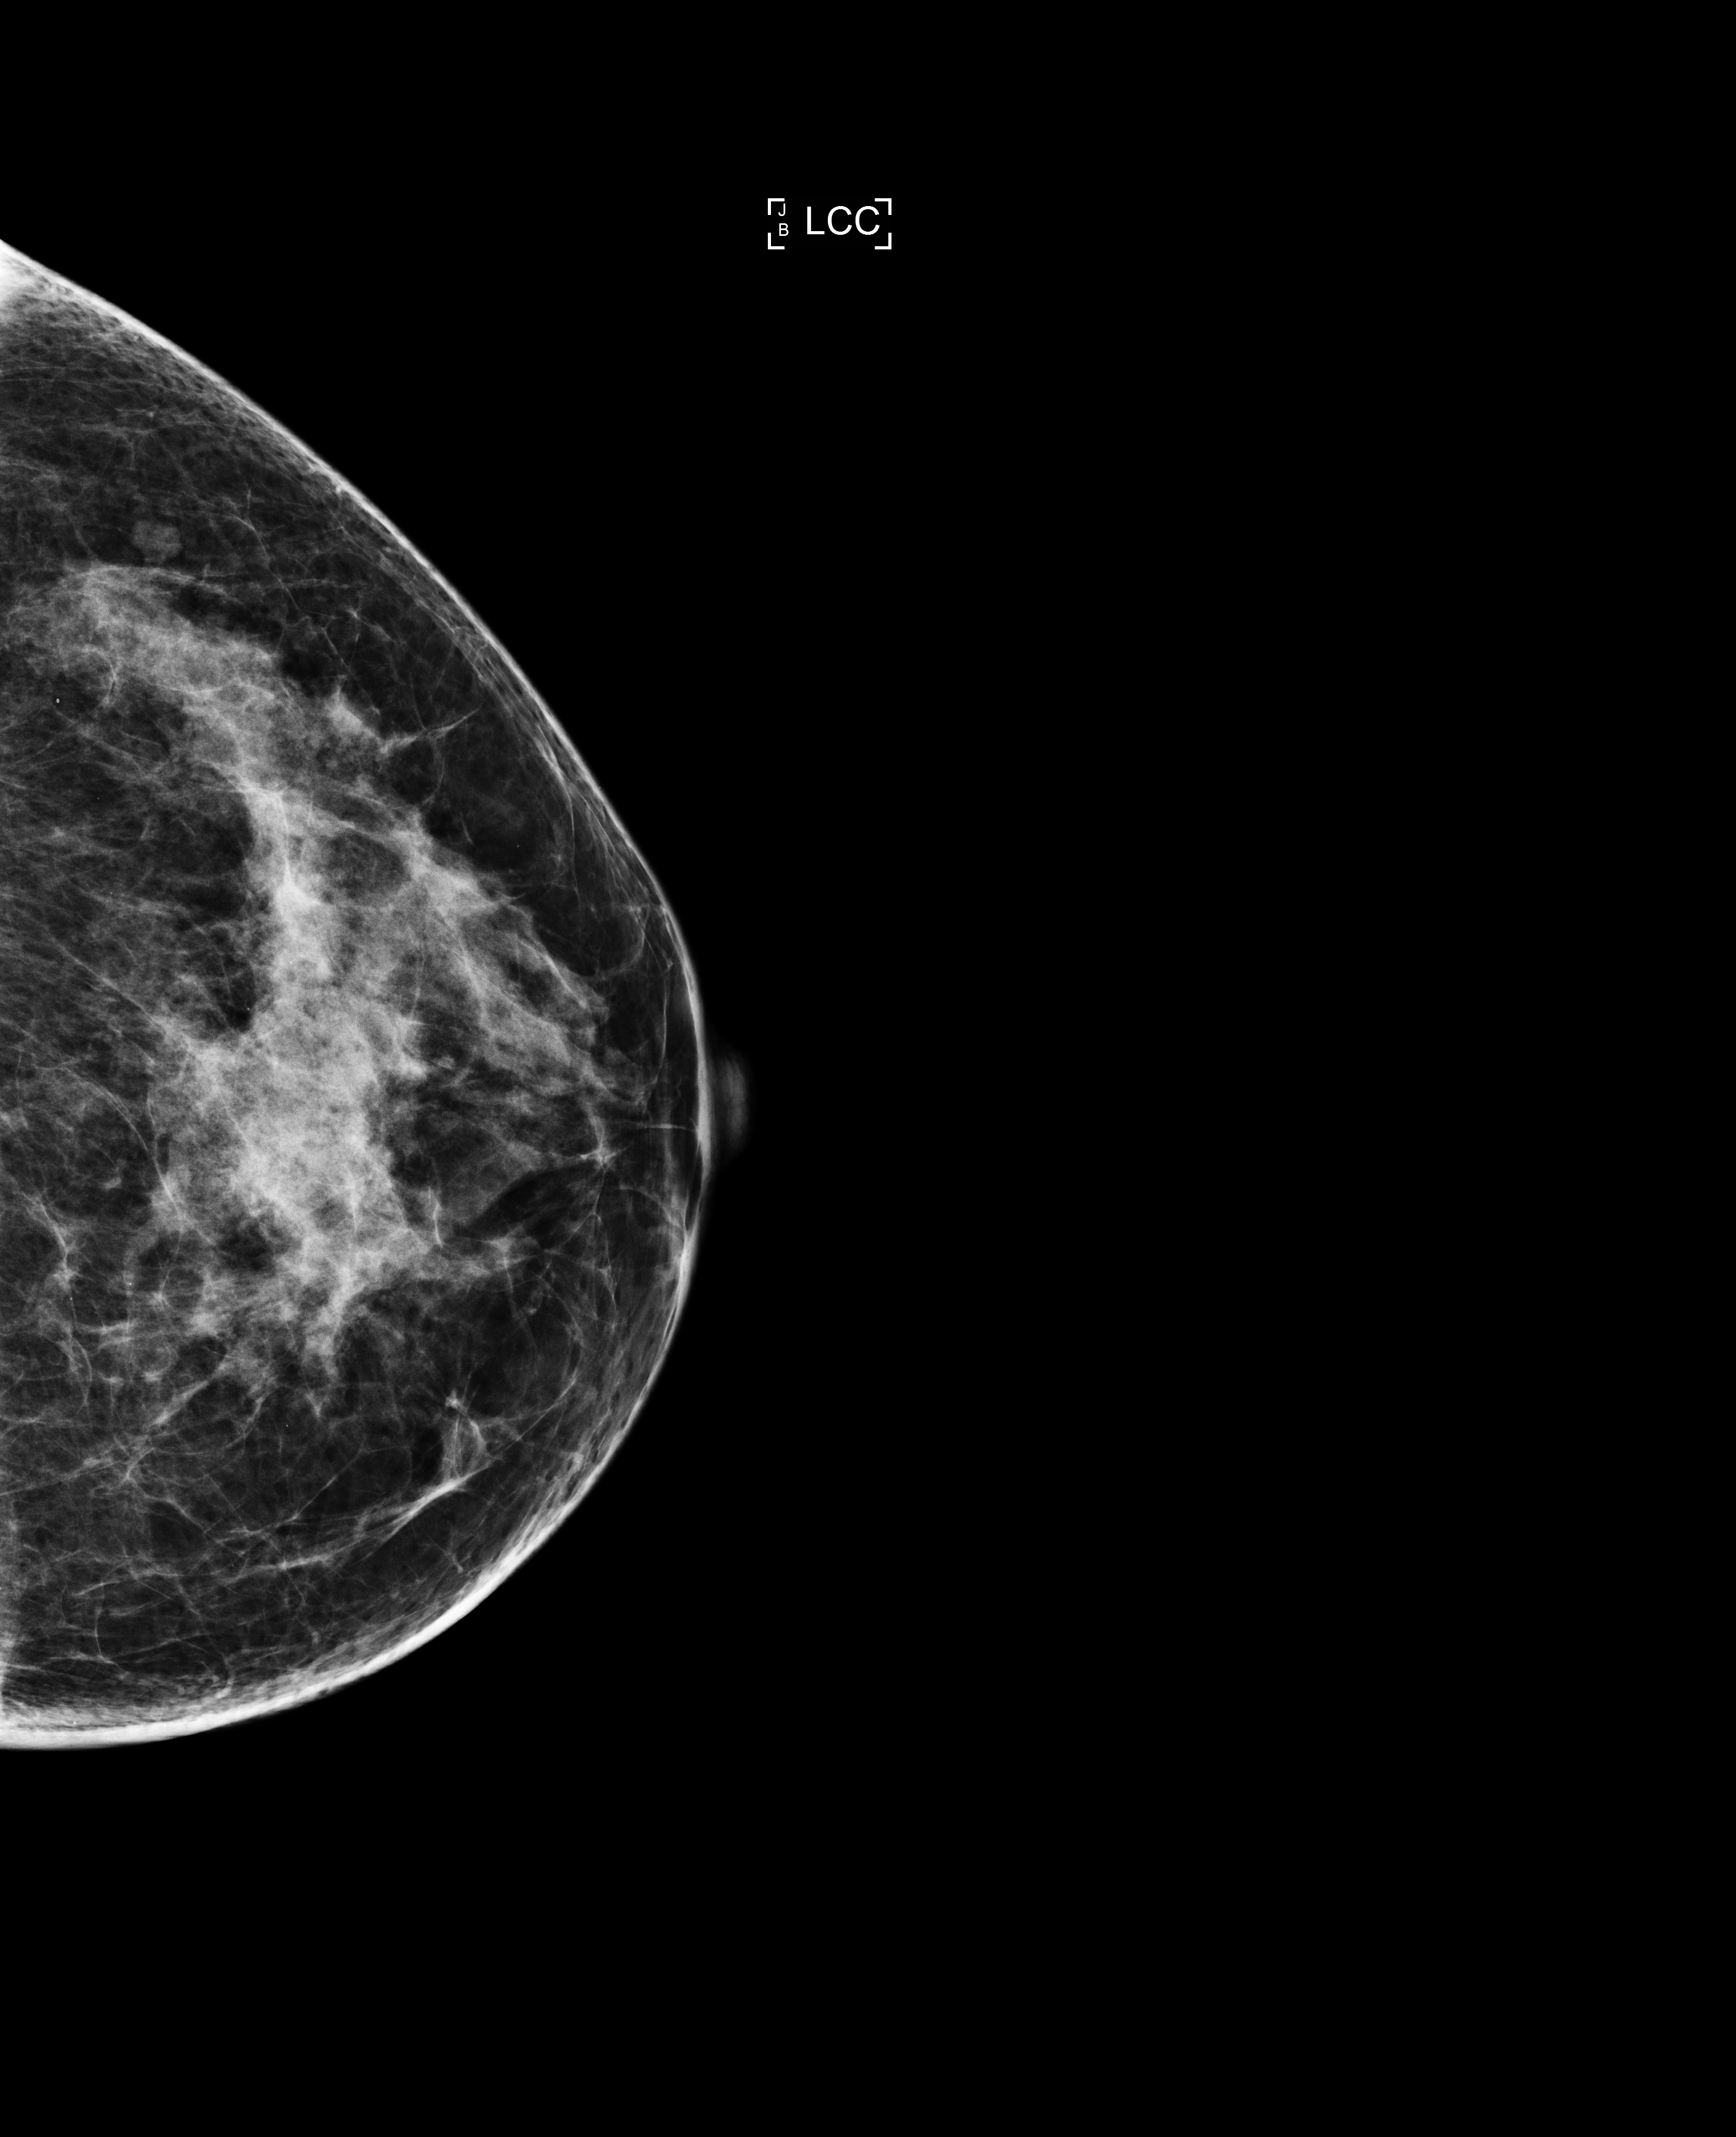
Annual screening mammography examination; compressed breast thickness 54 mm. Patient: female, 59 years.
Image type: full-field digital mammogram. Breast: left. Projection: cranio-caudal projection.